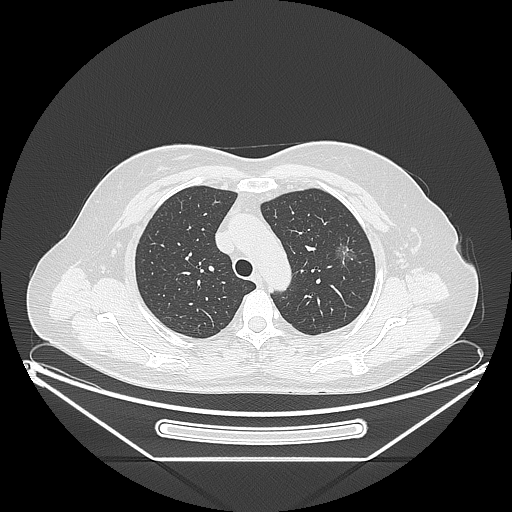
Chest CT, one axial slice. Slice 165 of 226 in the series (ordered by position). Lung window (W 1500 / L -600 HU). 512 × 512 image matrix, field of view 447 × 447 mm. Patient: female, 54 years. Case-level facts recorded for this patient, not image findings: clinical TNM (as recorded): T1c N0 M0; histopathological grade: G1.
Outlined on this slice (rectangle marked by the reading radiologist):
- lung tumour (recorded histology: adenocarcinoma): bounding box <330,236,357,270> (left, top, right, bottom; pixels)